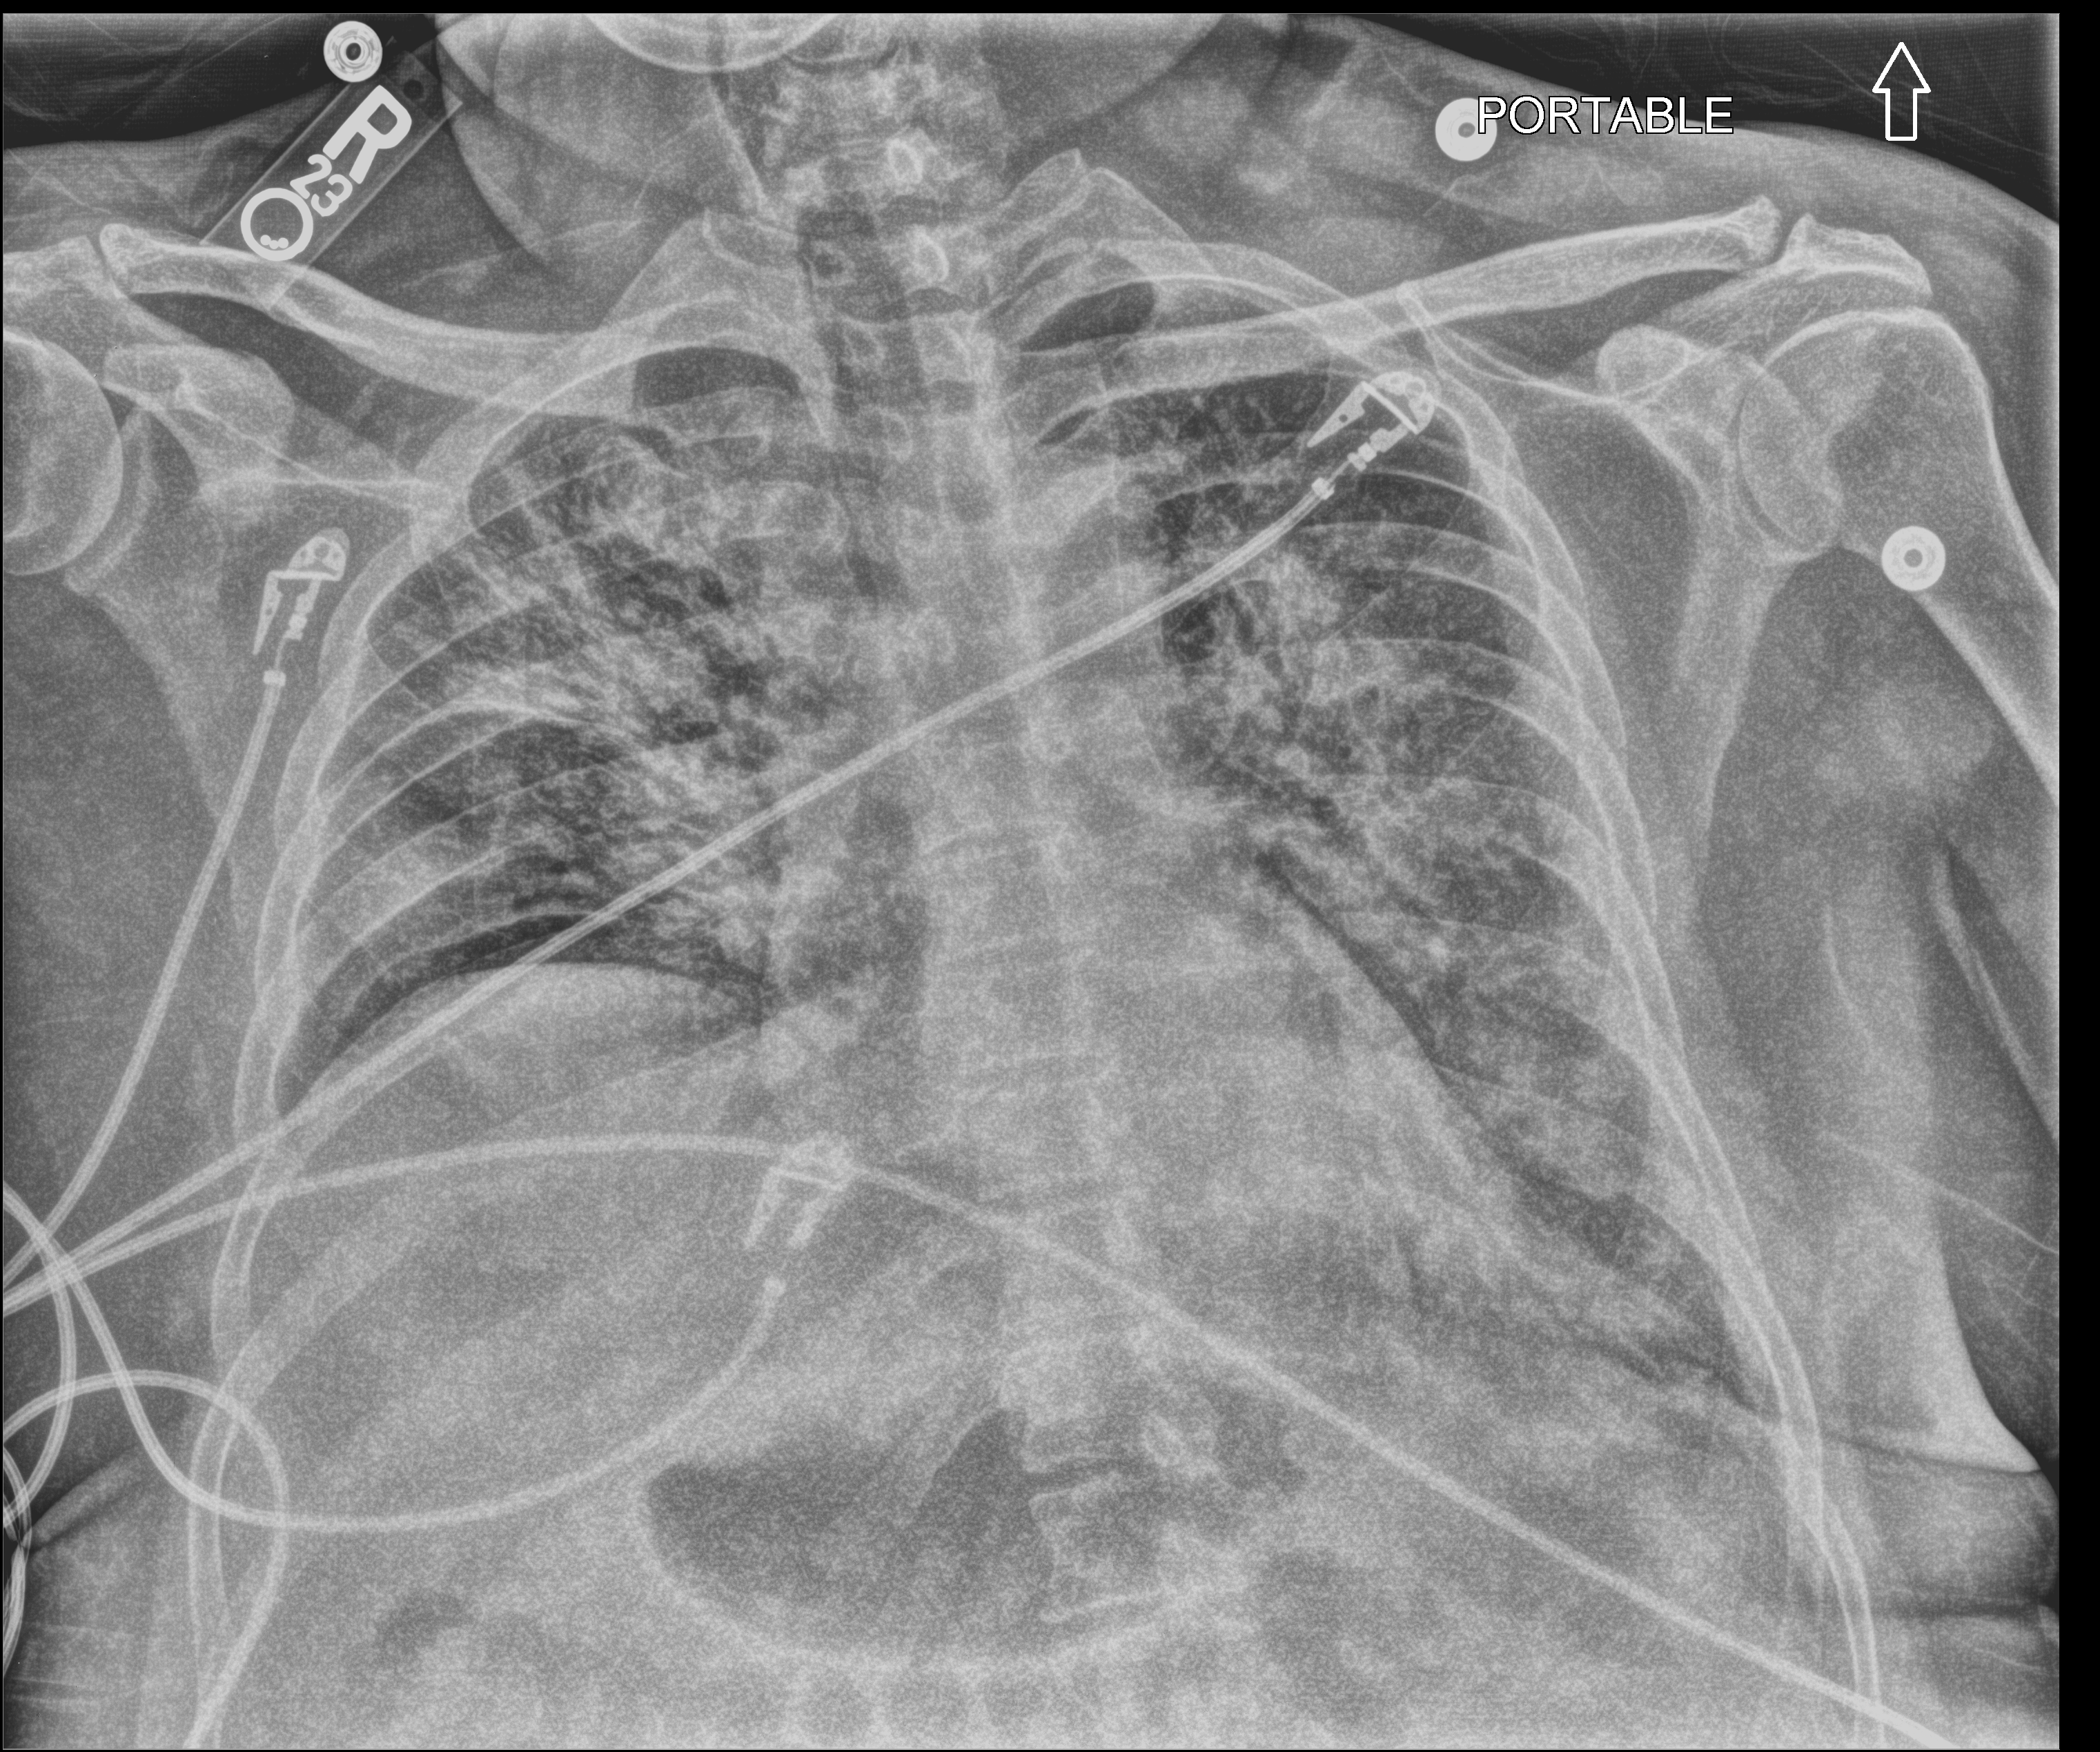
Bedside chest radiograph (computed radiography), anteroposterior (AP) projection. Patient hospitalised with COVID-19; male, aged 18–59 years.
Admission-level facts for this patient (not findings on this image; timing relative to this image not recorded): mechanically ventilated during this hospital stay: yes.